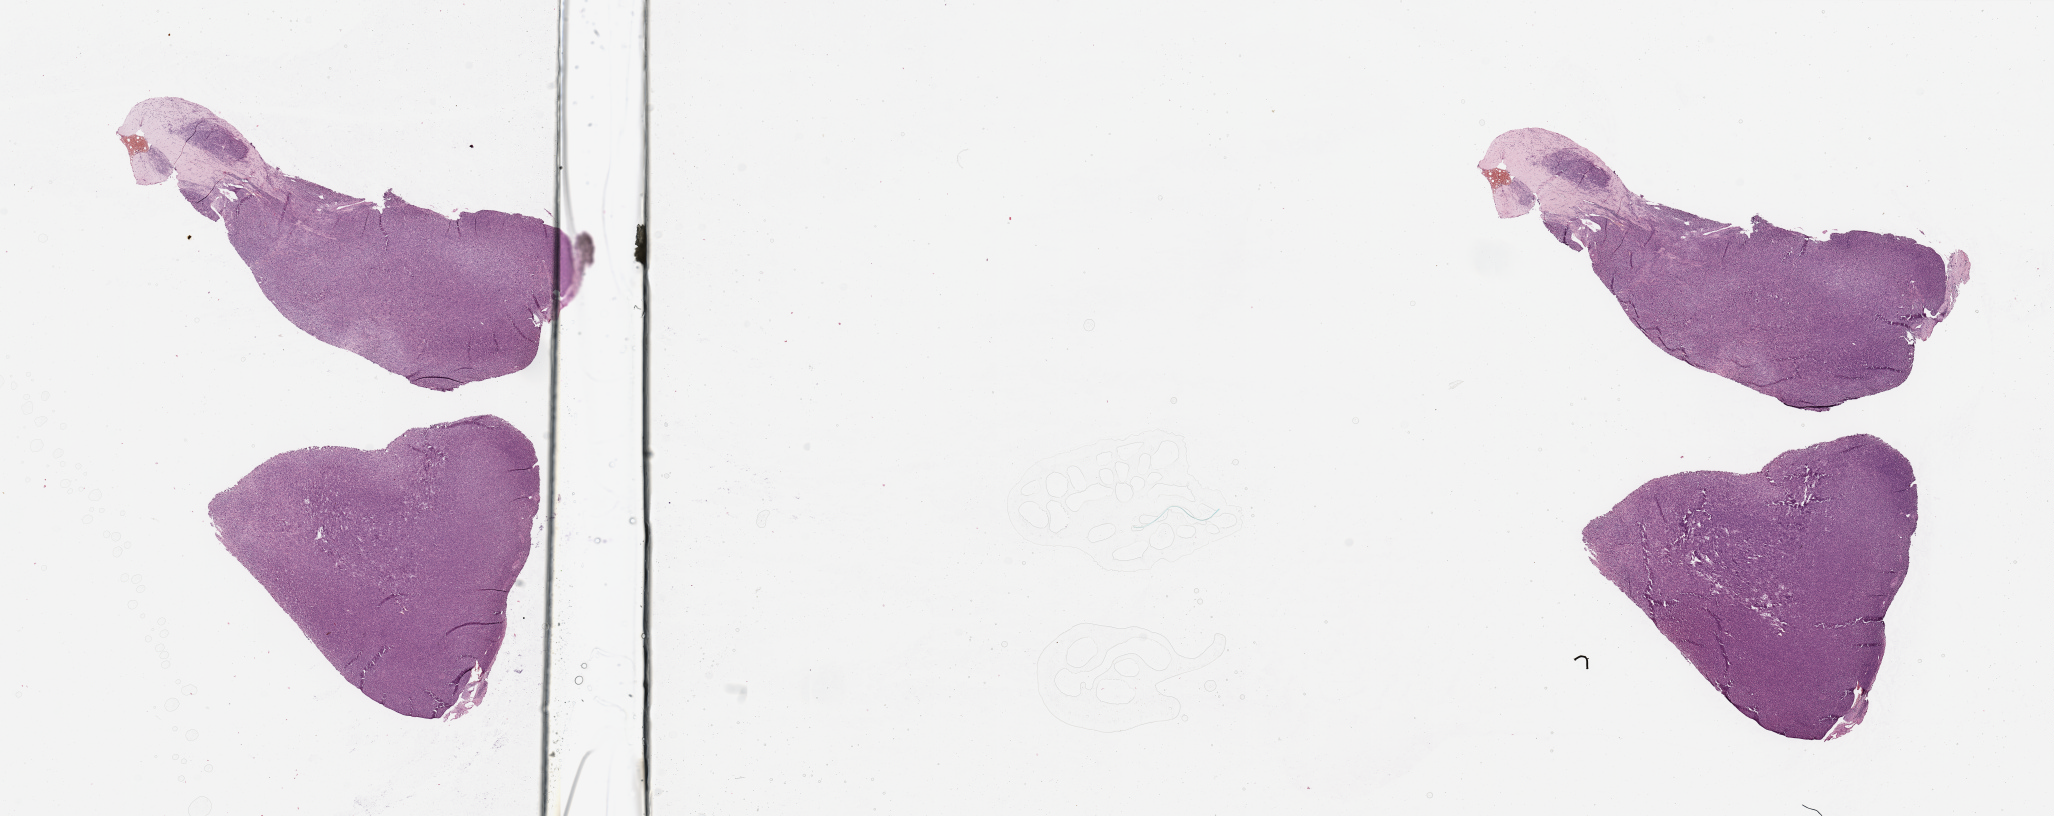
Digitized H&E-stained tissue section (whole slide), shown as a low-resolution overview of the whole scanned area (about 32.5 x 12.9 mm), tumour tissue sample. 52-year-old female patient.
Primary tumour site (as recorded): lower extremity. Patient diagnosis (cohort enrolment): sarcoma (site not recorded at cohort level).